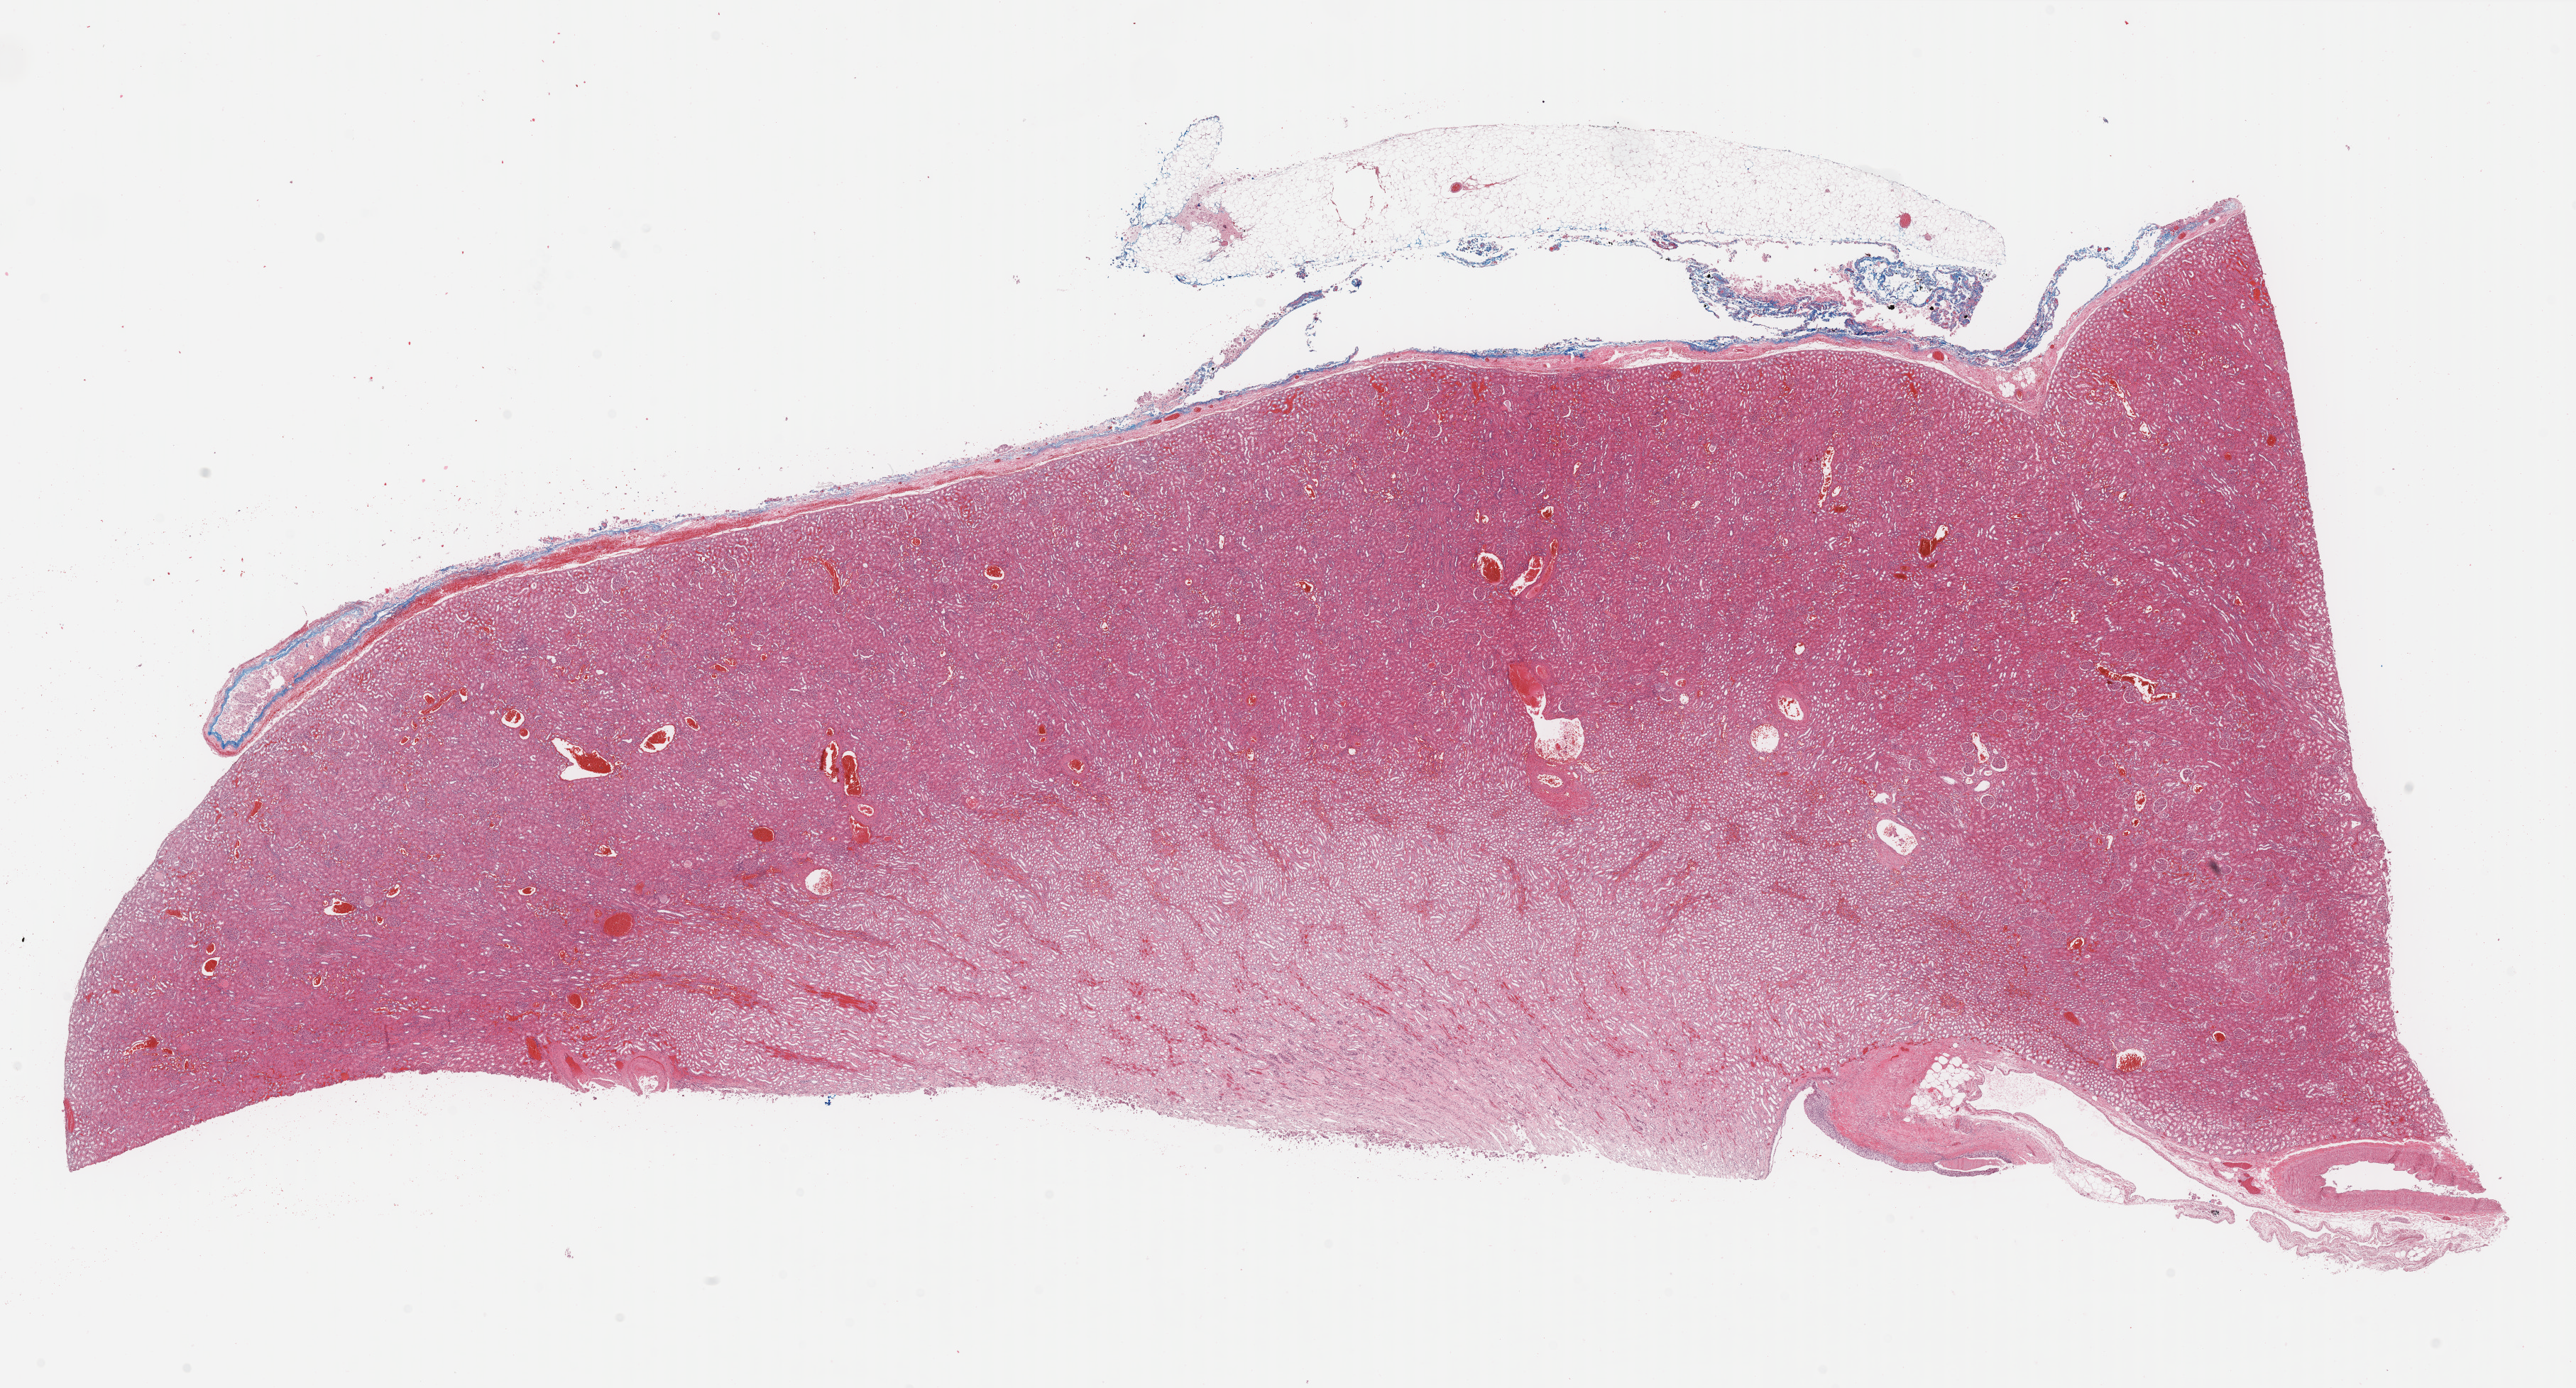
Digitized H&E-stained tissue section (whole slide) — a low-resolution overview of the entire scanned area, about 28.7 x 15.5 mm (acquisition: 40x scan); formalin-fixed paraffin-embedded (FFPE) diagnostic section; sample: solid tissue normal (non-tumour tissue), kidney. Patient: female, age at initial diagnosis 44 years.
This section: solid tissue normal sample (biorepository sample class). Patient diagnosis: Renal cell carcinoma, chromophobe type.